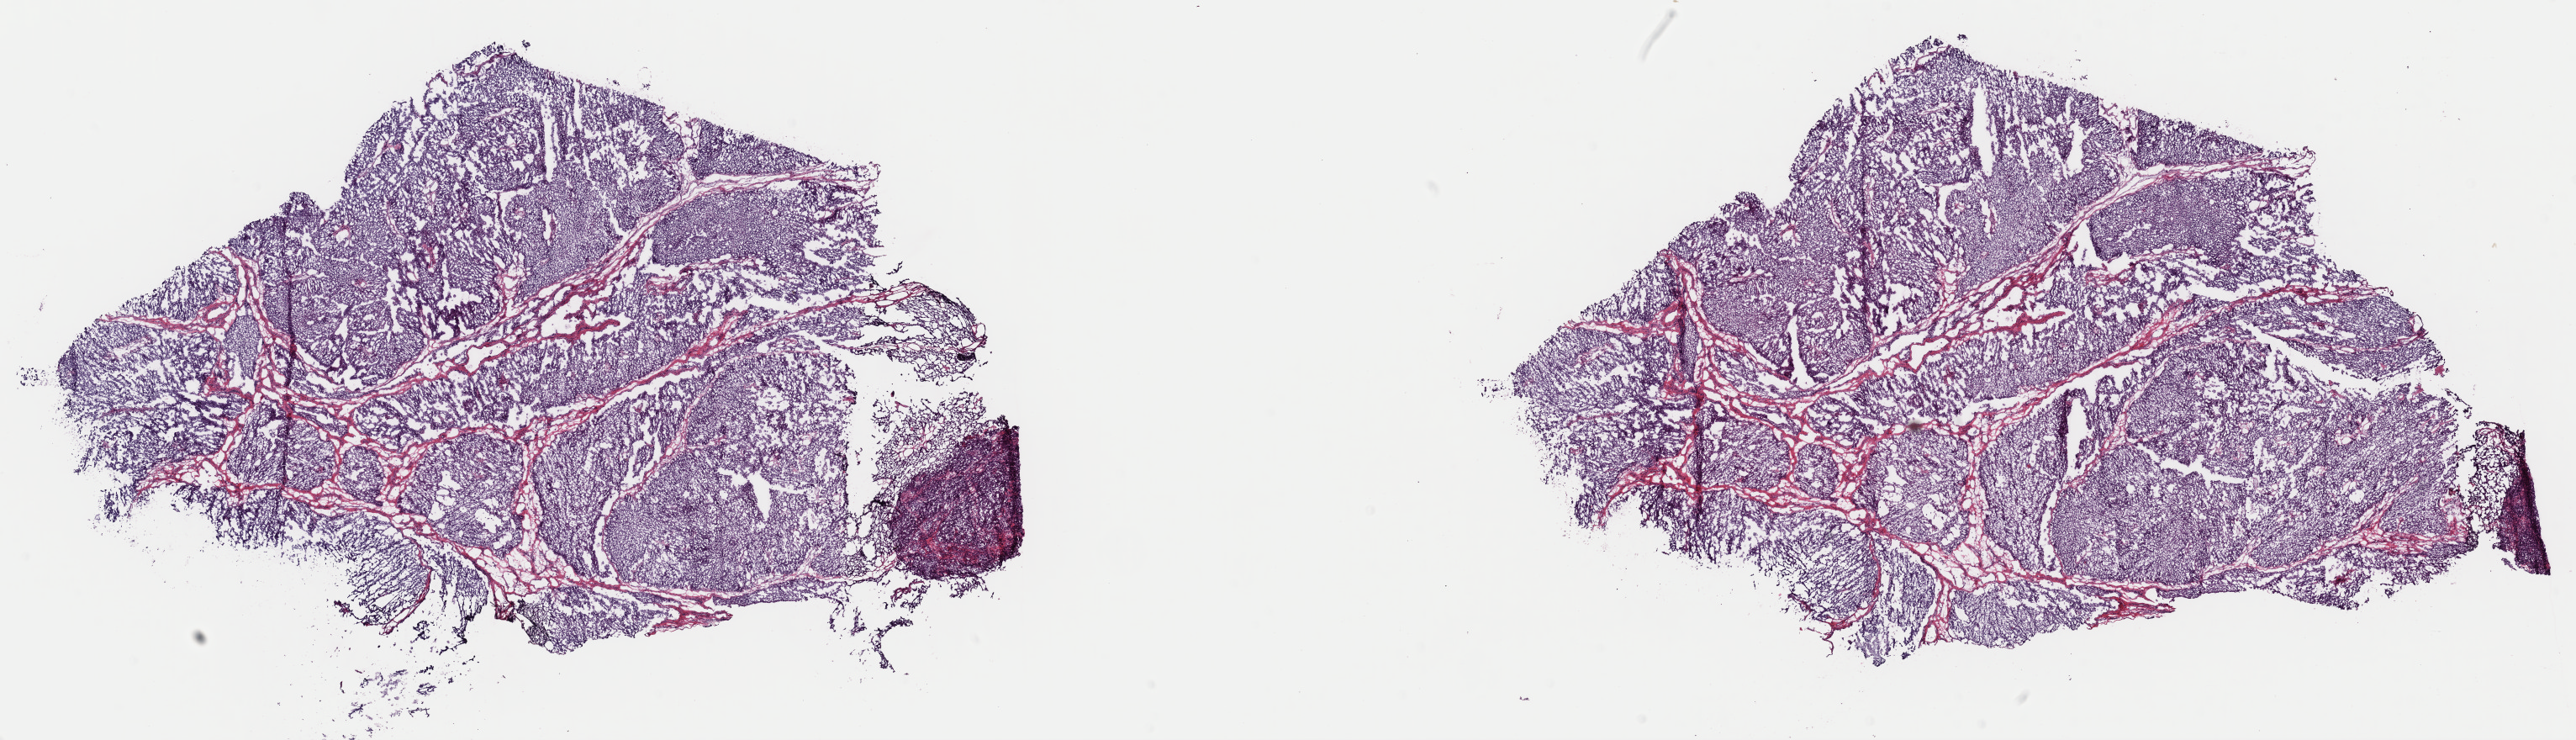
Digitized Hematoxylin and eosin (H&E) stained tissue section (whole slide) — shown as a low-resolution overview of the whole scanned area (about 24.2 x 7.0 mm, from a 40x scan), frozen section, primary tumour sample from the bladder. Male, age 57 years at initial diagnosis. Histologic grade: low grade. Pathologist review of this section (percent, as recorded): tumour cells 85%, tumour nuclei 95%, normal cells 0%, stromal cells 13%, necrosis 2%. Inflammatory infiltration, as recorded: lymphocyte infiltration 2%, monocyte infiltration 0%, neutrophil infiltration 0%.
Pathologic diagnosis: Transitional cell carcinoma. AJCC pathologic stage: II.